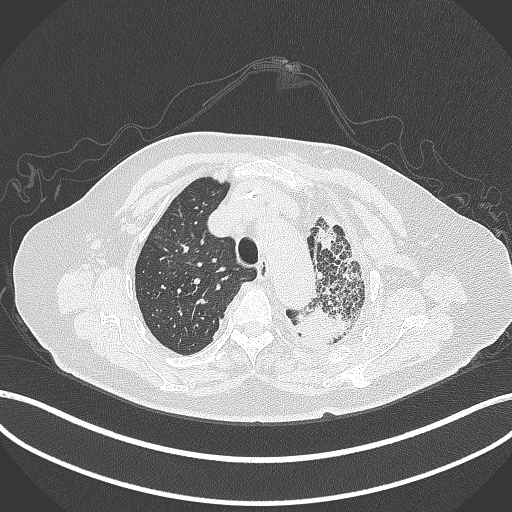
Chest CT, one axial slice; position 309 of 399 along the scan axis; reconstruction kernel B70f; 120 kVp; lung window (W 1500 / L -600 HU); 512 × 512 image matrix, field of view 400 × 400 mm. Patient: female, 75 years. Case-level facts recorded for this patient, not image findings: clinical TNM (as recorded): T3 N3 M1.
Structures marked on this image (rectangle marked by the reading radiologist):
- lung tumour (recorded histology: adenocarcinoma): bounding box (x1, y1, x2, y2) in pixels: (287, 300, 362, 350)